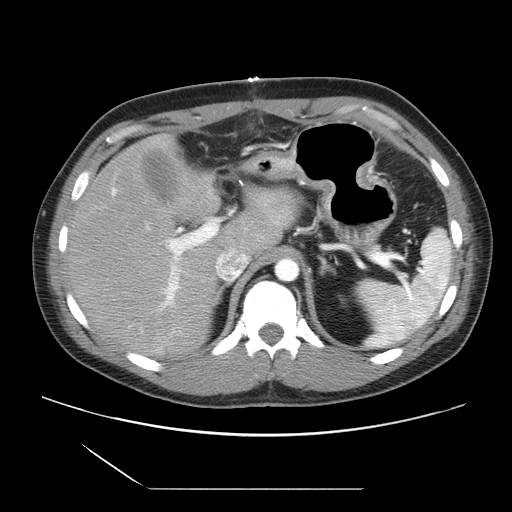
Contrast-enhanced abdominal CT, one axial slice; position 18 of 39 along the scan axis; intravenous contrast given; soft-tissue window (W 400 / L 40 HU); 512 × 512 image matrix, field of view 395 × 395 mm. Male patient, age 39 years. From the clinical record (not read from this slice): diagnosis: colorectal cancer liver metastases, imaged before liver resection; multiple liver metastases: yes; largest metastasis: 1.3 cm.
Annotated regions visible in this slice (manually delineated by an expert):
- hepatic veins: bounding box [x1, y1, x2, y2] px = [185, 248, 248, 282]
- liver: [66, 136, 295, 358]
- planned liver remnant (the part of the liver to remain after resection): [119, 136, 296, 255]
- portal vein (with intrahepatic branches): [111, 186, 217, 312]